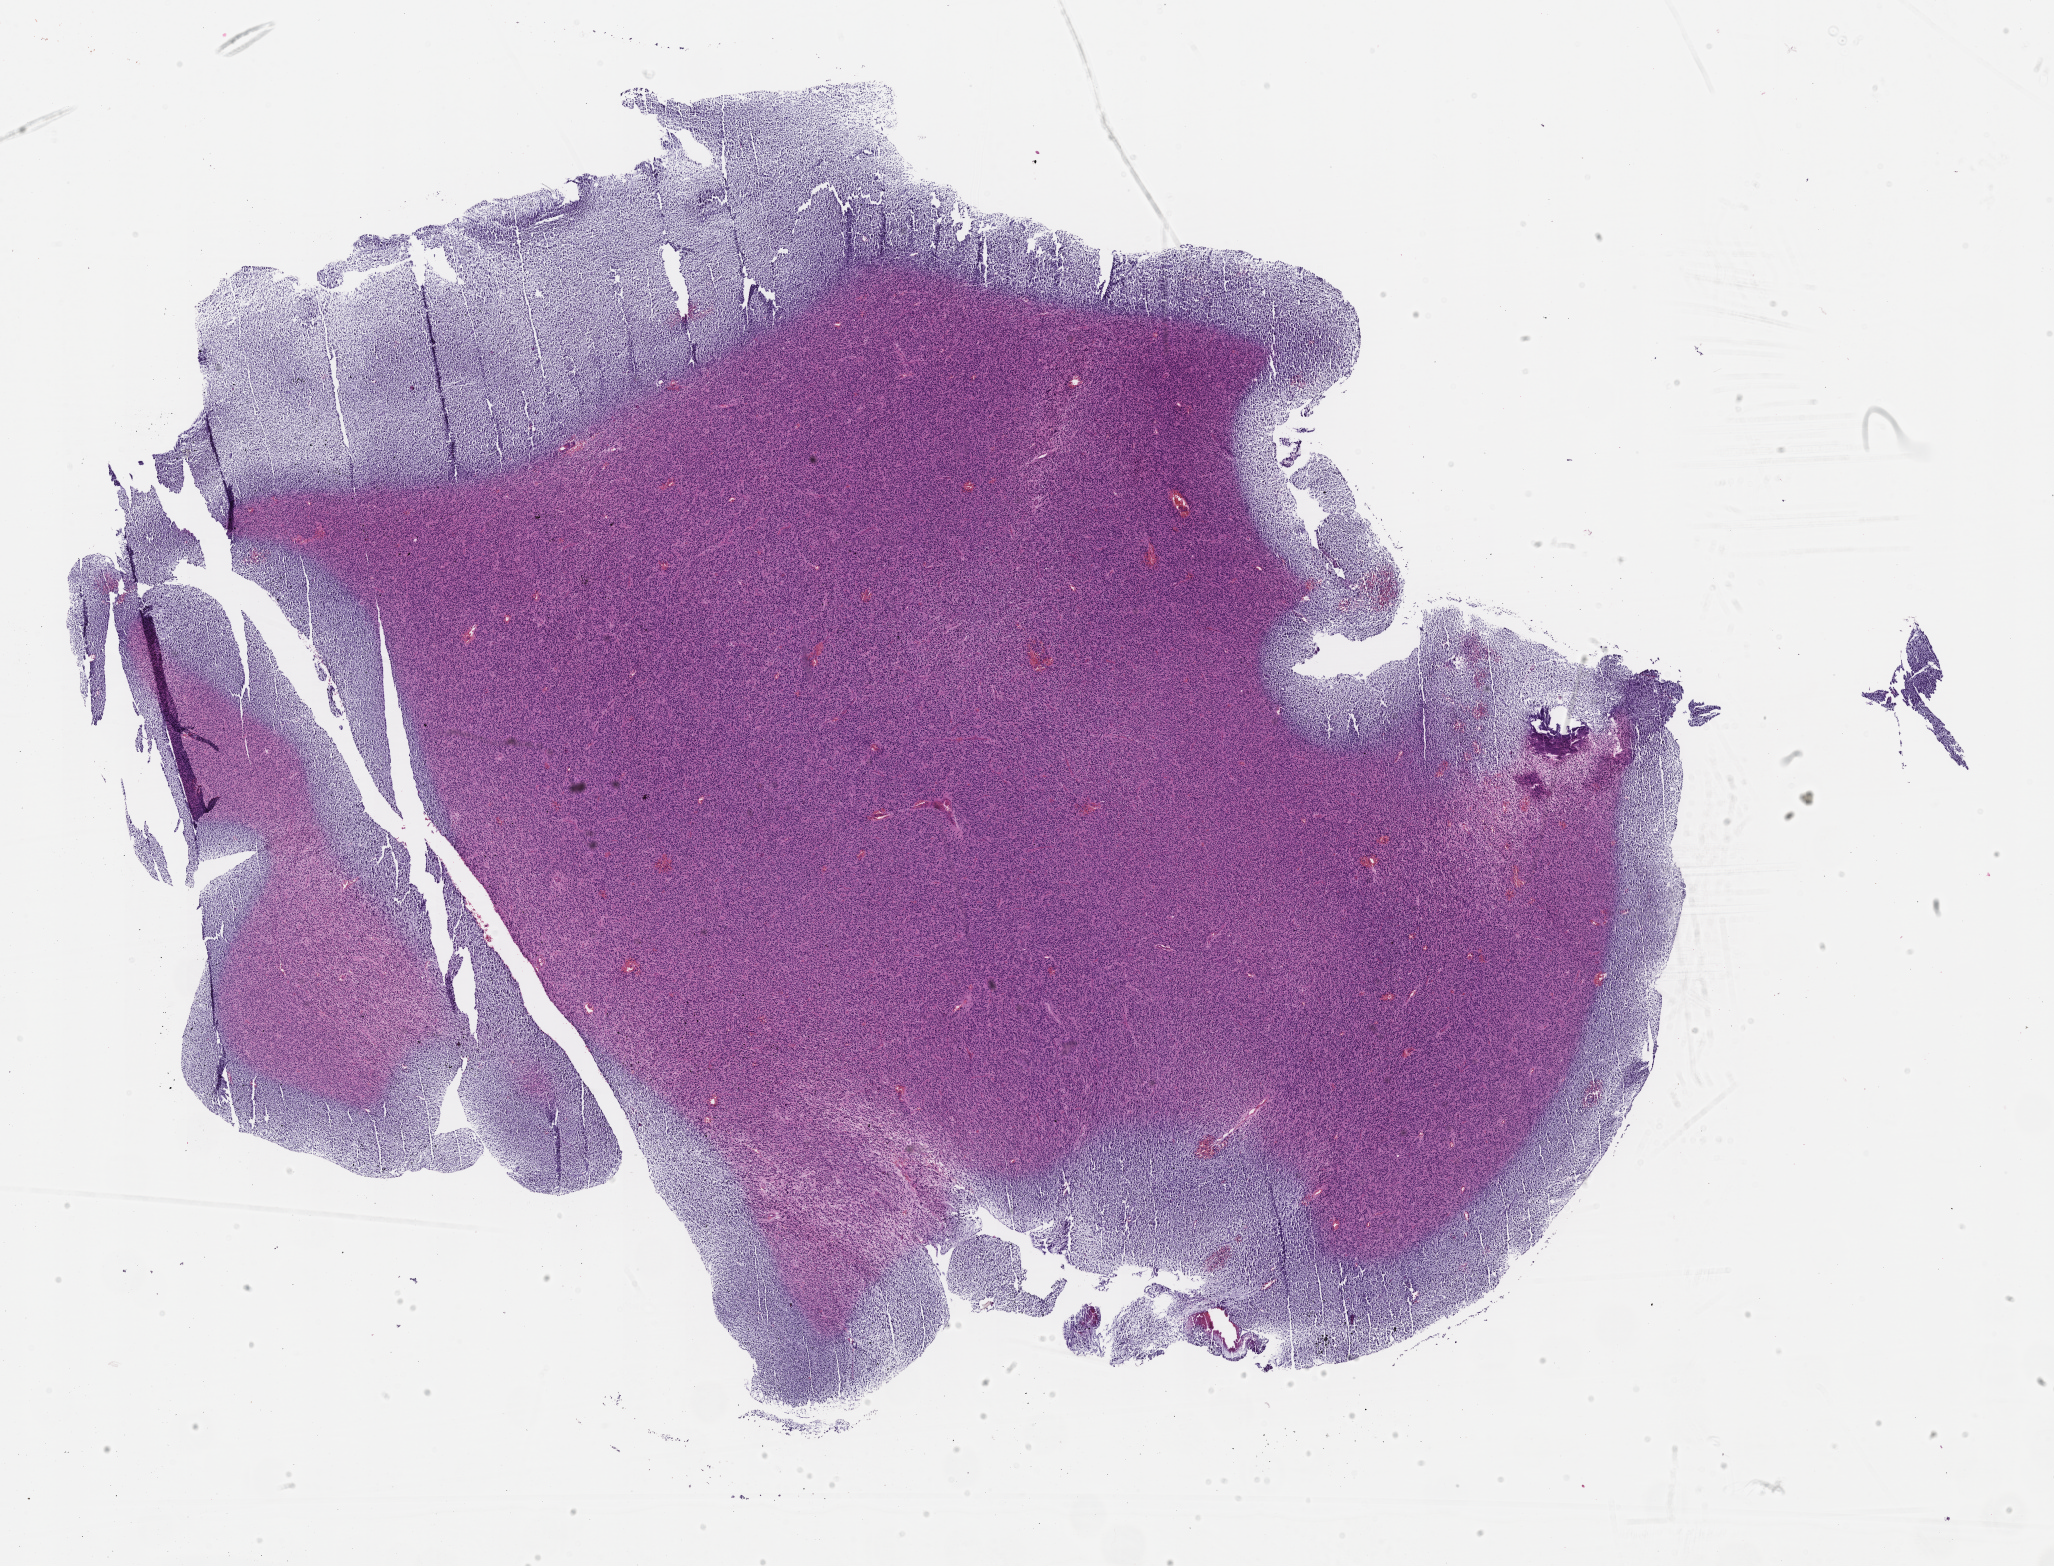
Digitized Hematoxylin and eosin (H&E) stained tissue section (whole slide), shown as a low-resolution overview of the whole scanned area (about 16.7 x 12.7 mm), formalin-fixed paraffin-embedded (FFPE) diagnostic section, sample: primary tumour, brain. Male patient; age at initial diagnosis 57 years.
* pathologic diagnosis: Glioblastoma